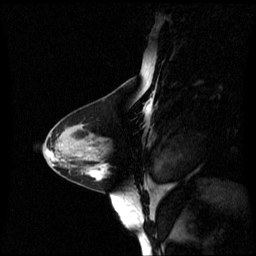
Breast MRI (dynamic contrast-enhanced), one sagittal slice; slice 27 of 60 in the series (ordered by position); dynamic contrast-enhanced series, image 2 of 3 at this slice position (ordered by acquisition); 1.5 T; TE 4.2 ms, TR 8.4 ms; 2.4 mm slice thickness; 256 × 256 image matrix, field of view 250 × 250 mm. Patient: female, 44 years. From the clinical record (not read from this slice): setting: breast cancer imaged before/during neoadjuvant chemotherapy; receptor status: triple-negative.
Annotated regions visible in this slice (semi-automatically segmented with operator editing):
- analysis volume of interest (the breast-tissue region the enhancement analysis was run in; not a lesion): bounding box (x1, y1, x2, y2) in pixels: (79, 148, 132, 190)
- tumour enhancement mask (voxels above the 70 % enhancement threshold inside the analysis volume of interest): (93, 166, 108, 177)